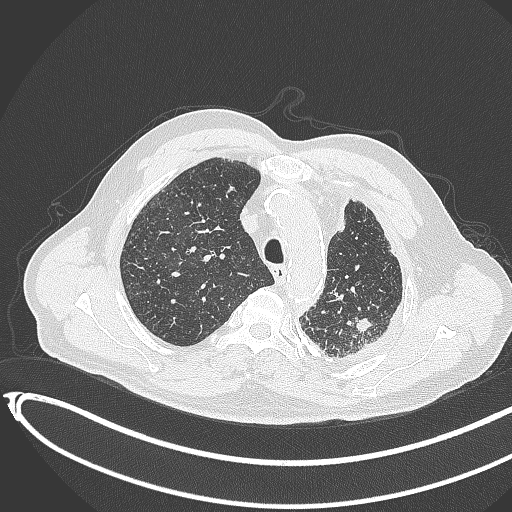
Chest CT, one axial slice; slice 335 of 451 in the series (ordered by position); reconstruction kernel B70f; 120 kVp; lung window (W 1500 / L -600 HU); 1 mm slice thickness; 512 × 512 image matrix, field of view 400 × 400 mm. Patient: male, 78 years. Case-level facts recorded for this patient, not image findings: clinical TNM (as recorded): T1c N0 M1.
Structures marked on this image (bounding box drawn by a radiologist):
- lung tumour (recorded histology: adenocarcinoma): box from (x=355, y=313) to (x=376, y=334) px